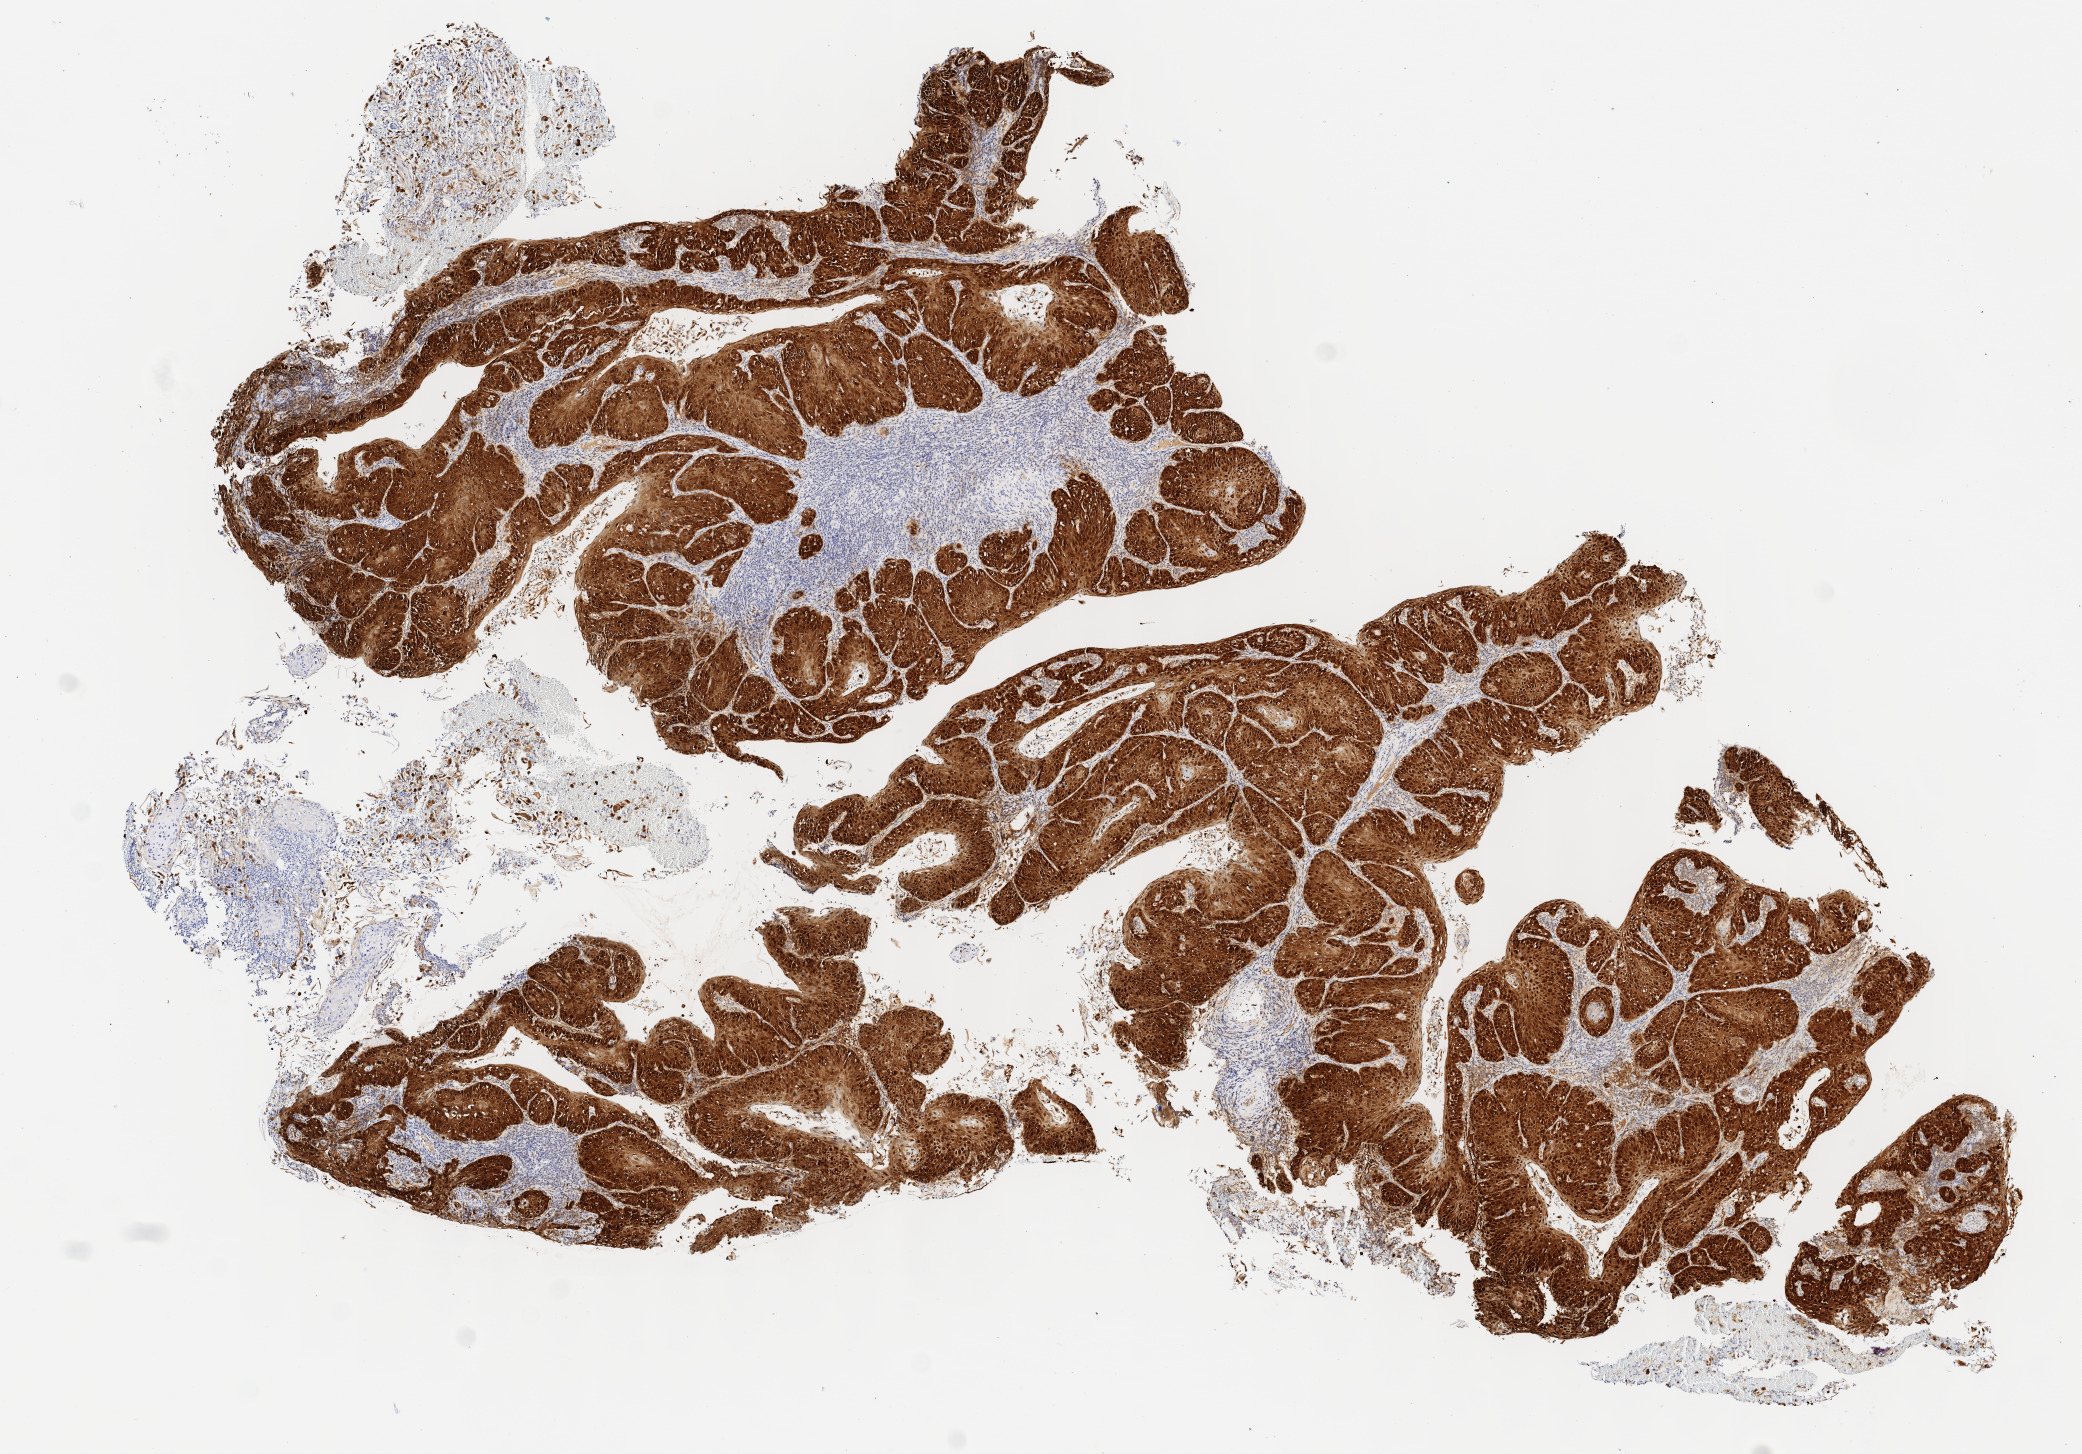
Whole-slide image, immunohistochemical stain for p16 (p16INK4a), a low-resolution overview of the entire scanned area, about 8.3 x 5.8 mm, specimen: tumor tissue, site: cervix. Patient: female, age 41 years.
Diagnosis: Squamous cell carcinoma, keratinizing, NOS.